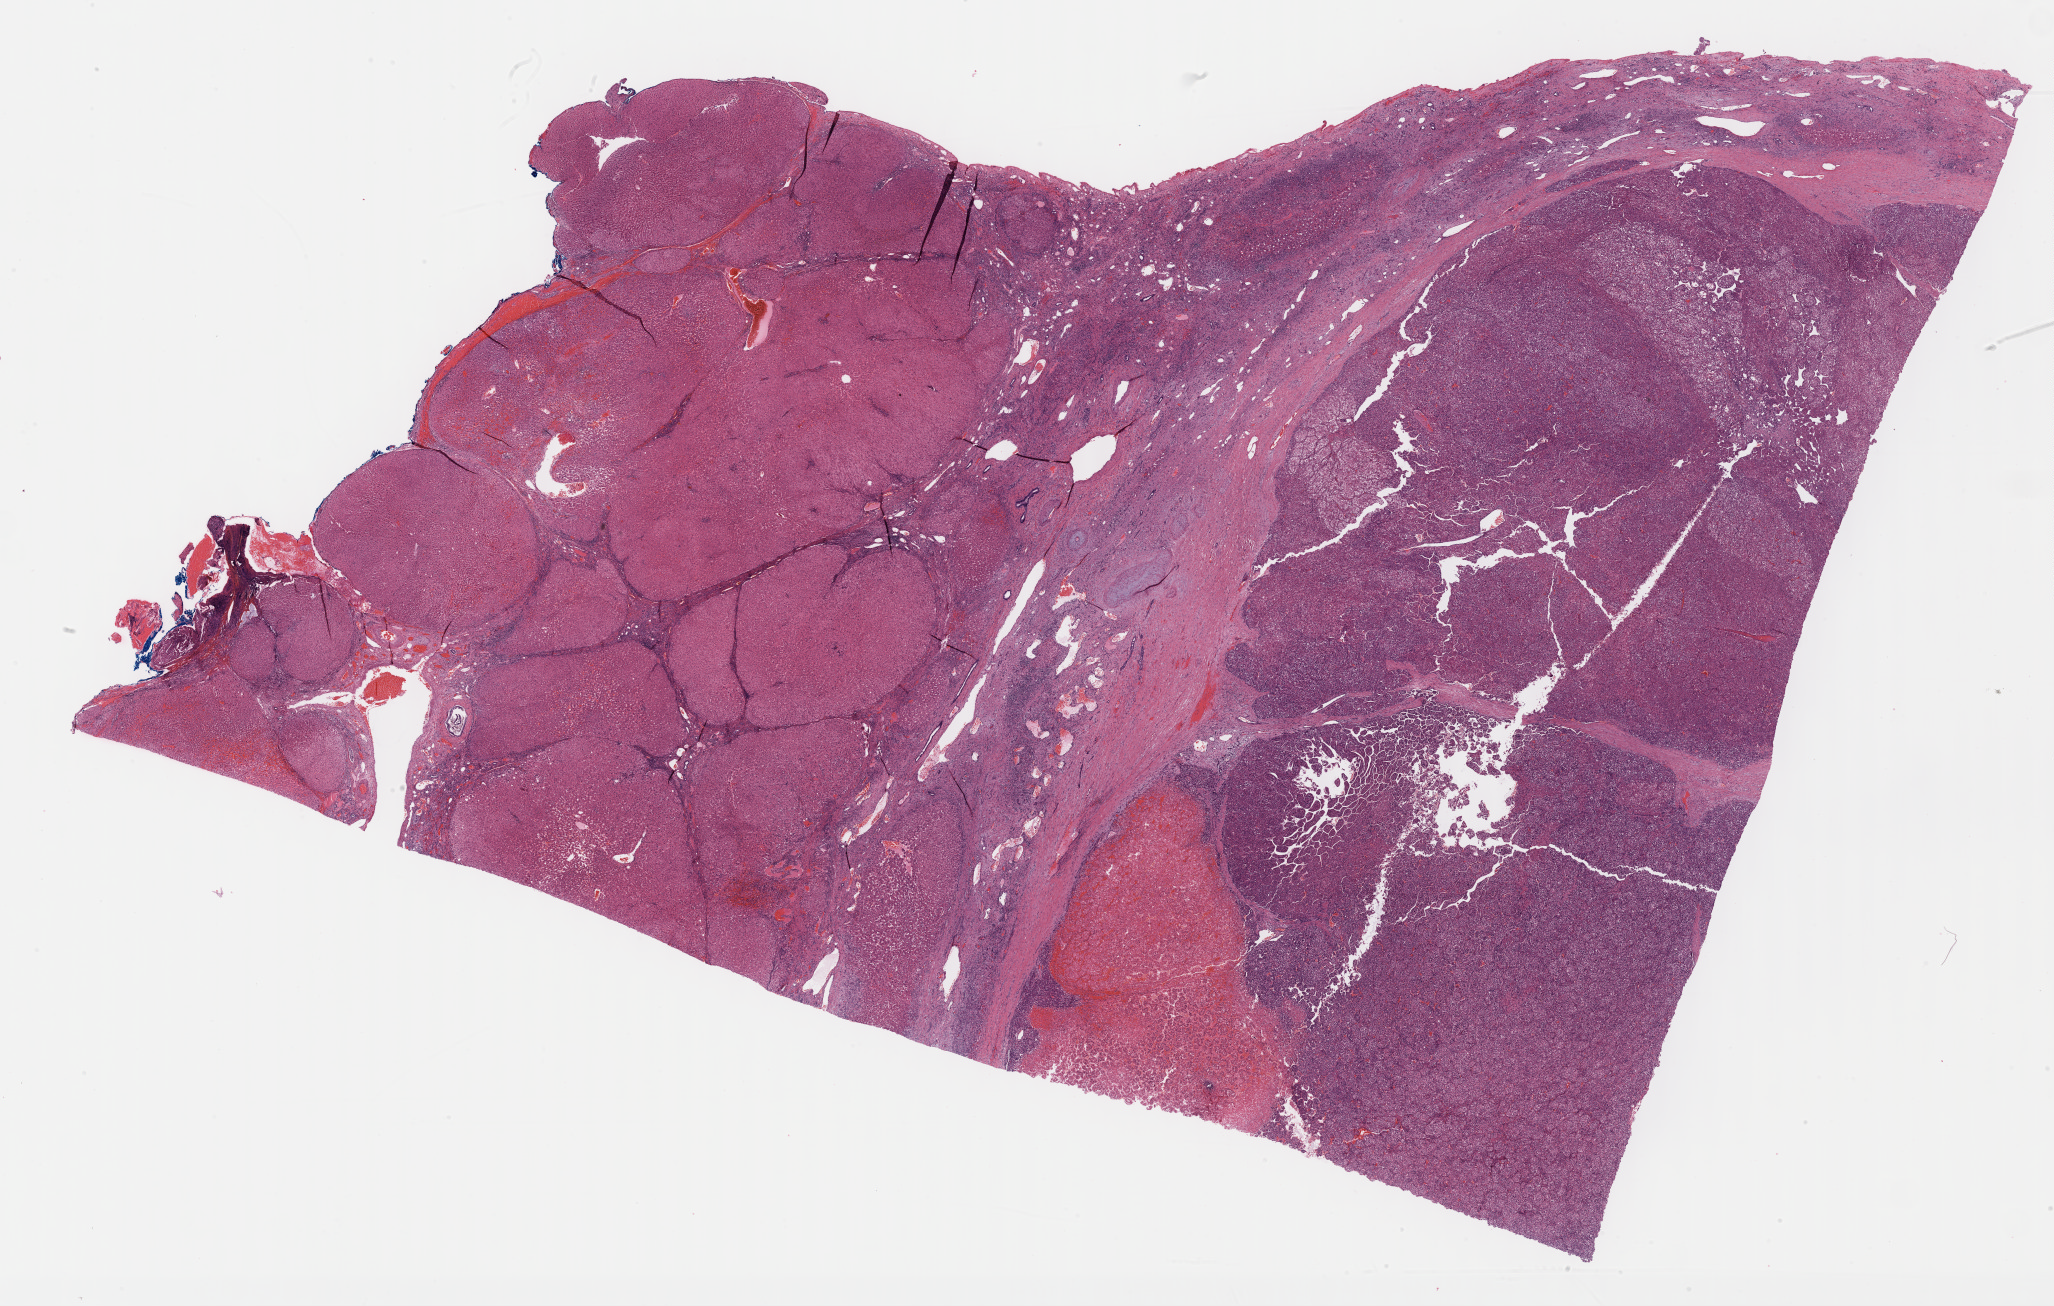
H&E whole-slide image, shown as a low-resolution overview of the whole scanned area (about 33.2 x 21.1 mm, slide scanned at 40x); formalin-fixed paraffin-embedded (FFPE) diagnostic section; primary tumour sample from the liver. Patient: male, age at initial diagnosis 51 years. Histologic grade: G3 (poorly differentiated).
AJCC pathologic stage: IIIC (7th edition). TNM: T4 N0 M0. Diagnosis: Hepatocellular carcinoma, NOS.